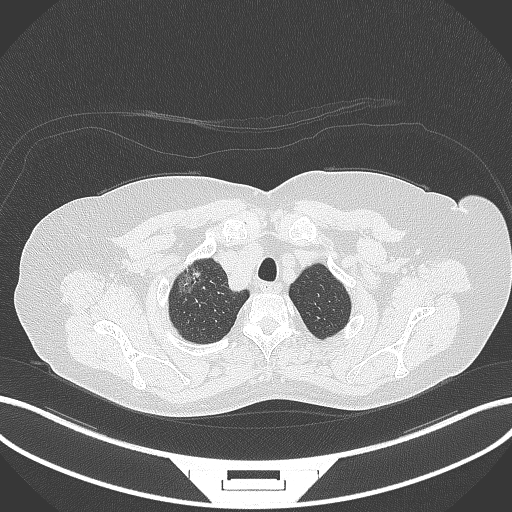
Chest CT, one axial slice. 120 kVp. Lung window (W 1500 / L -600 HU). 1 mm slice thickness. 512 × 512 image matrix, field of view 400 × 400 mm. Female patient, age 62 years. Case-level facts recorded for this patient, not image findings: clinical TNM (as recorded): T1c N0 M0.
Structures marked on this image (rectangle marked by the reading radiologist):
- lung tumour (recorded histology: adenocarcinoma): bounding box <179,265,208,298> (left, top, right, bottom; pixels)